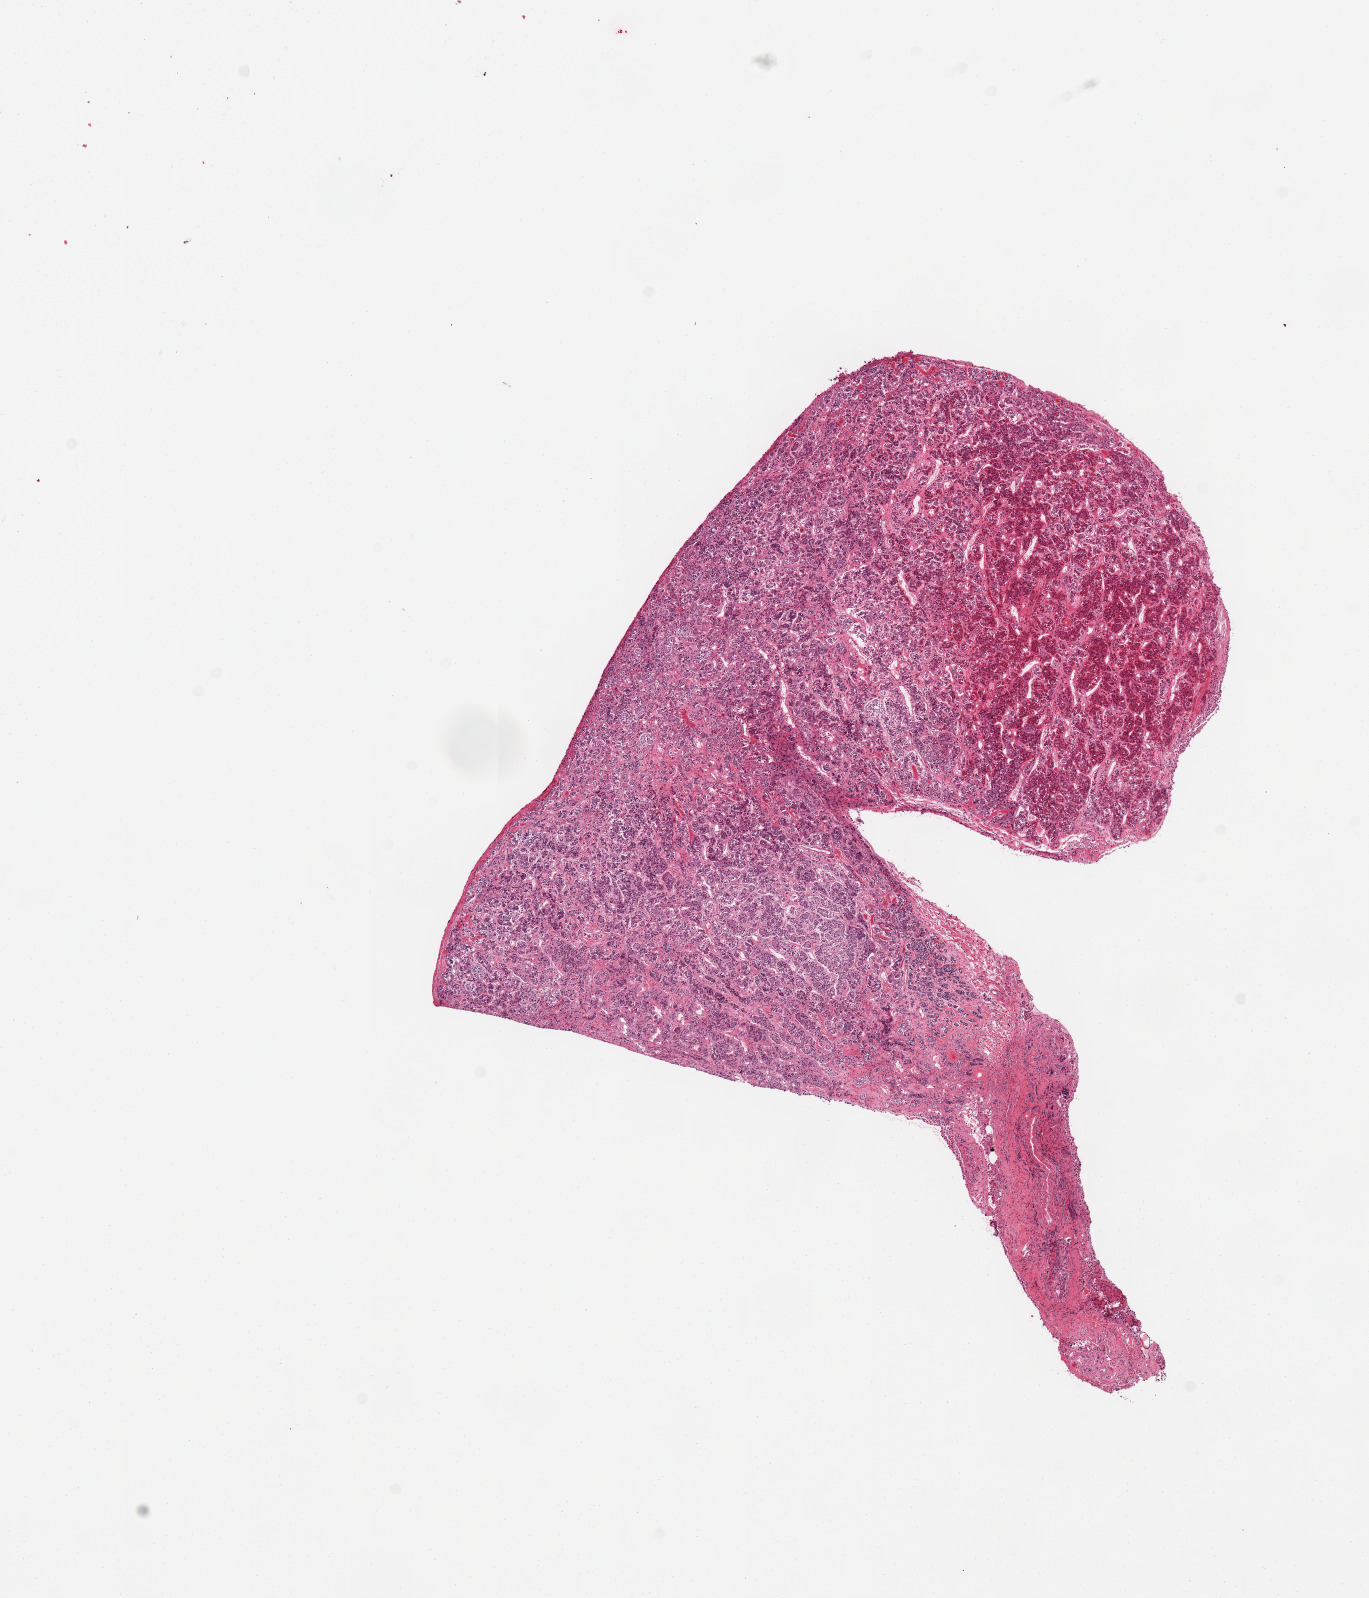
Whole-slide image, haematoxylin and eosin stain, shown as a low-resolution overview of the whole scanned area (about 10.8 x 12.6 mm); PAXgene-fixed, paraffin-embedded tissue; section of pituitary (target tissue); tissue donor sample.
Review note (as recorded): 1 piece; anterior present.